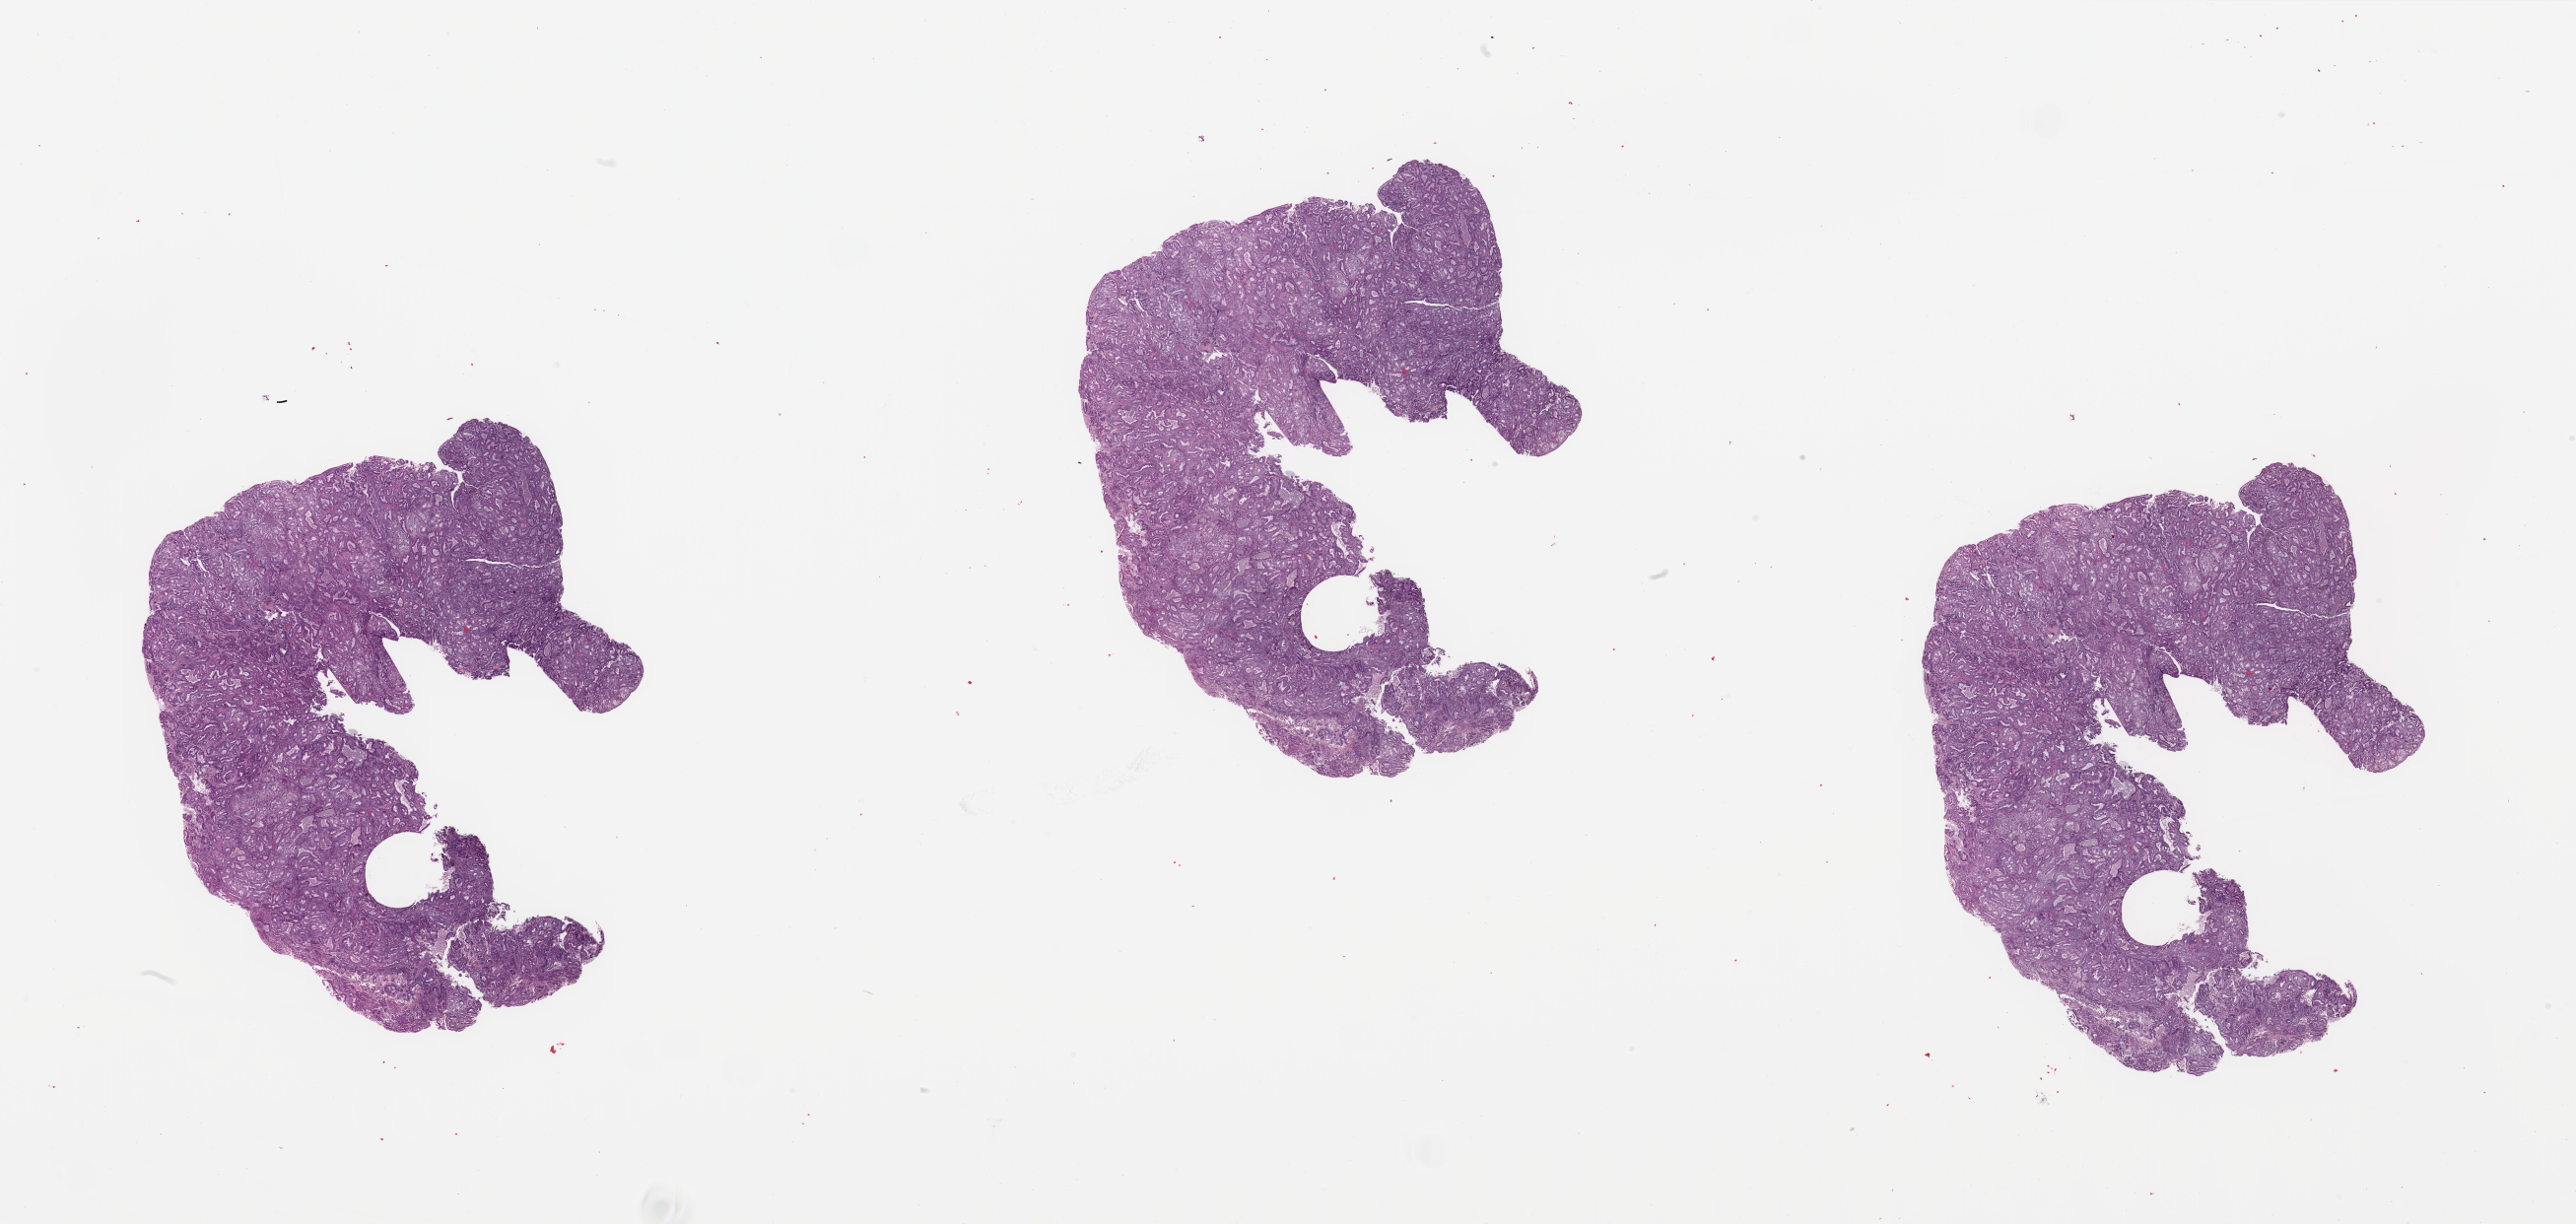
H&E-stained whole-slide image, whole scanned area (about 41.3 x 19.6 mm, acquisition: 20x scan) shown as a low-resolution overview, uterus, tumour tissue. 72-year-old female patient. Histologic grade: G2 (moderately differentiated).
• histologic diagnosis: Endometrioid adenocarcinoma, NOS
• AJCC pathologic stage: I